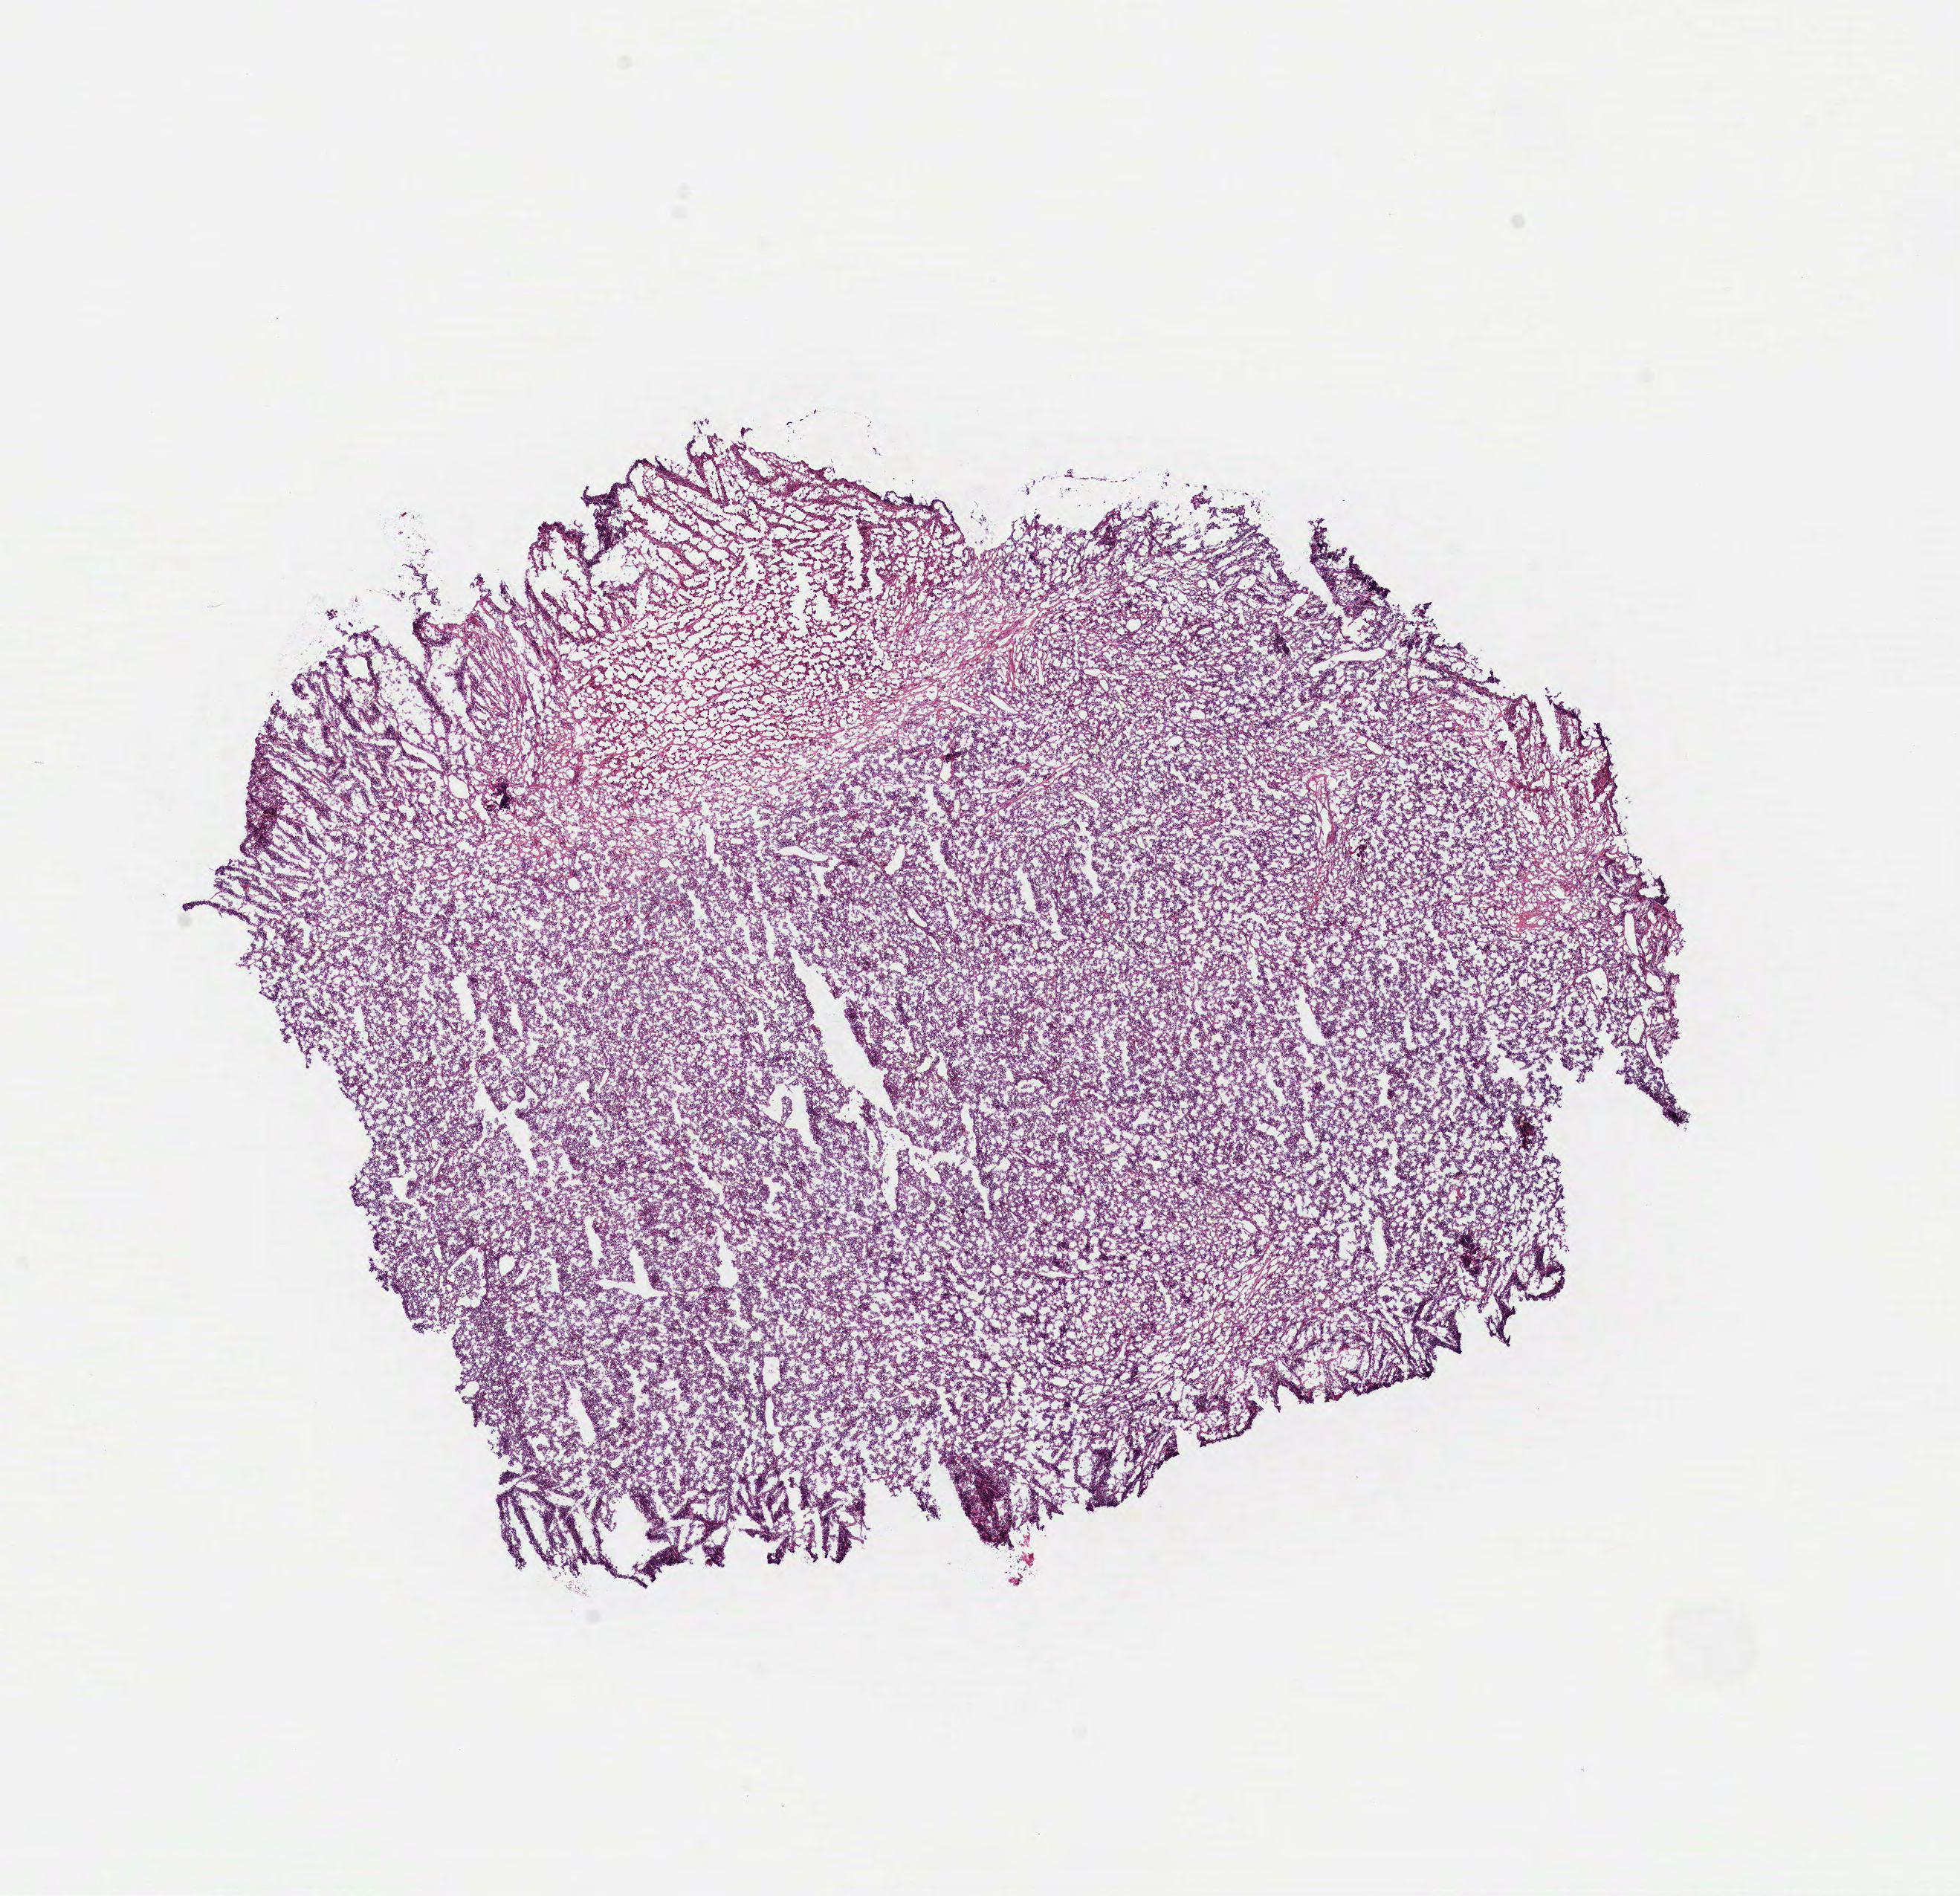
Hematoxylin and eosin (H&E) stained whole-slide image, shown as a low-resolution overview of the whole scanned area (about 10.6 x 10.3 mm). Frozen section from the bottom of the tissue portion. Sample: primary tumour, lymphoid tissue. Patient: male, age at initial diagnosis 58 years. Slide review estimates, as recorded: tumour cells 85%, tumour nuclei 80%, normal cells 0%, stromal cells 0%, necrosis 15%. Infiltration values recorded for this section: lymphocyte infiltration 80%, monocyte infiltration 0%, neutrophil infiltration 0%.
Diagnosis: Diffuse large B-cell lymphoma, NOS.